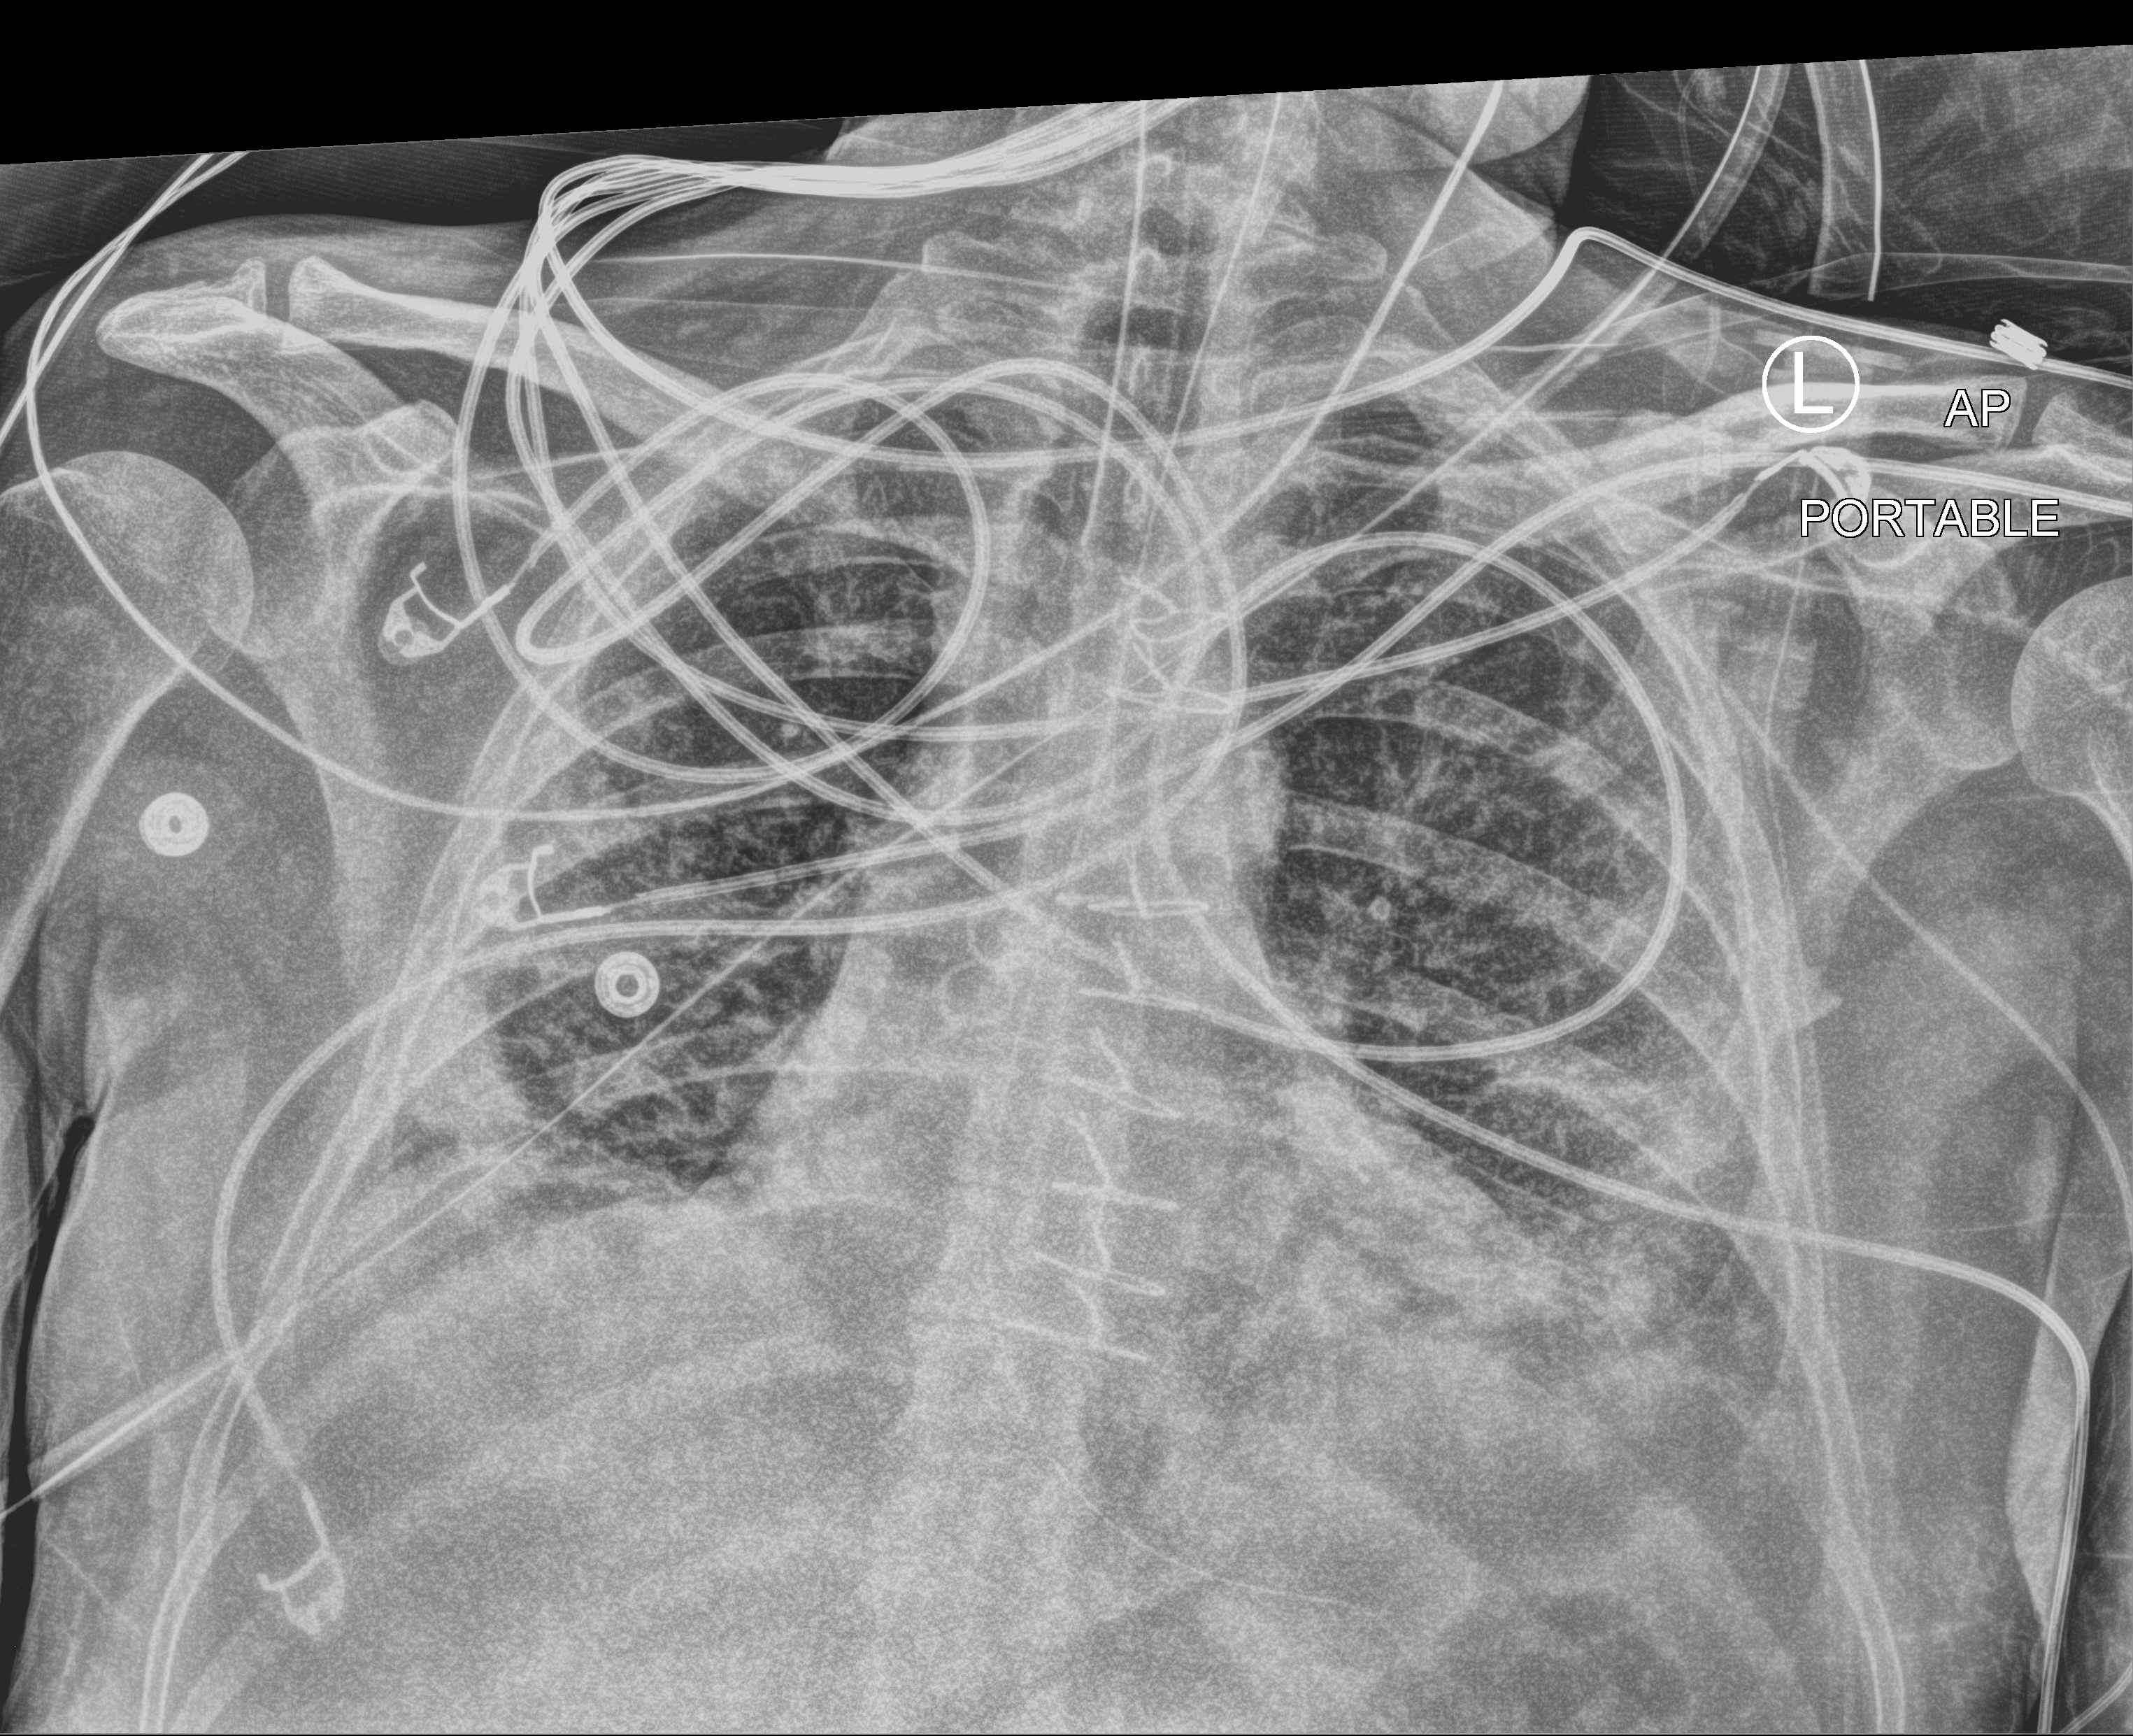
Portable chest radiograph, anteroposterior (AP) projection. Patient hospitalised with COVID-19; male, aged 18–59 years.
Hospital-stay facts (about this admission, not read from this image; timing relative to this image not recorded): length of hospital stay: 63 days; smoking status (admission record): former; mechanically ventilated during this hospital stay: yes.